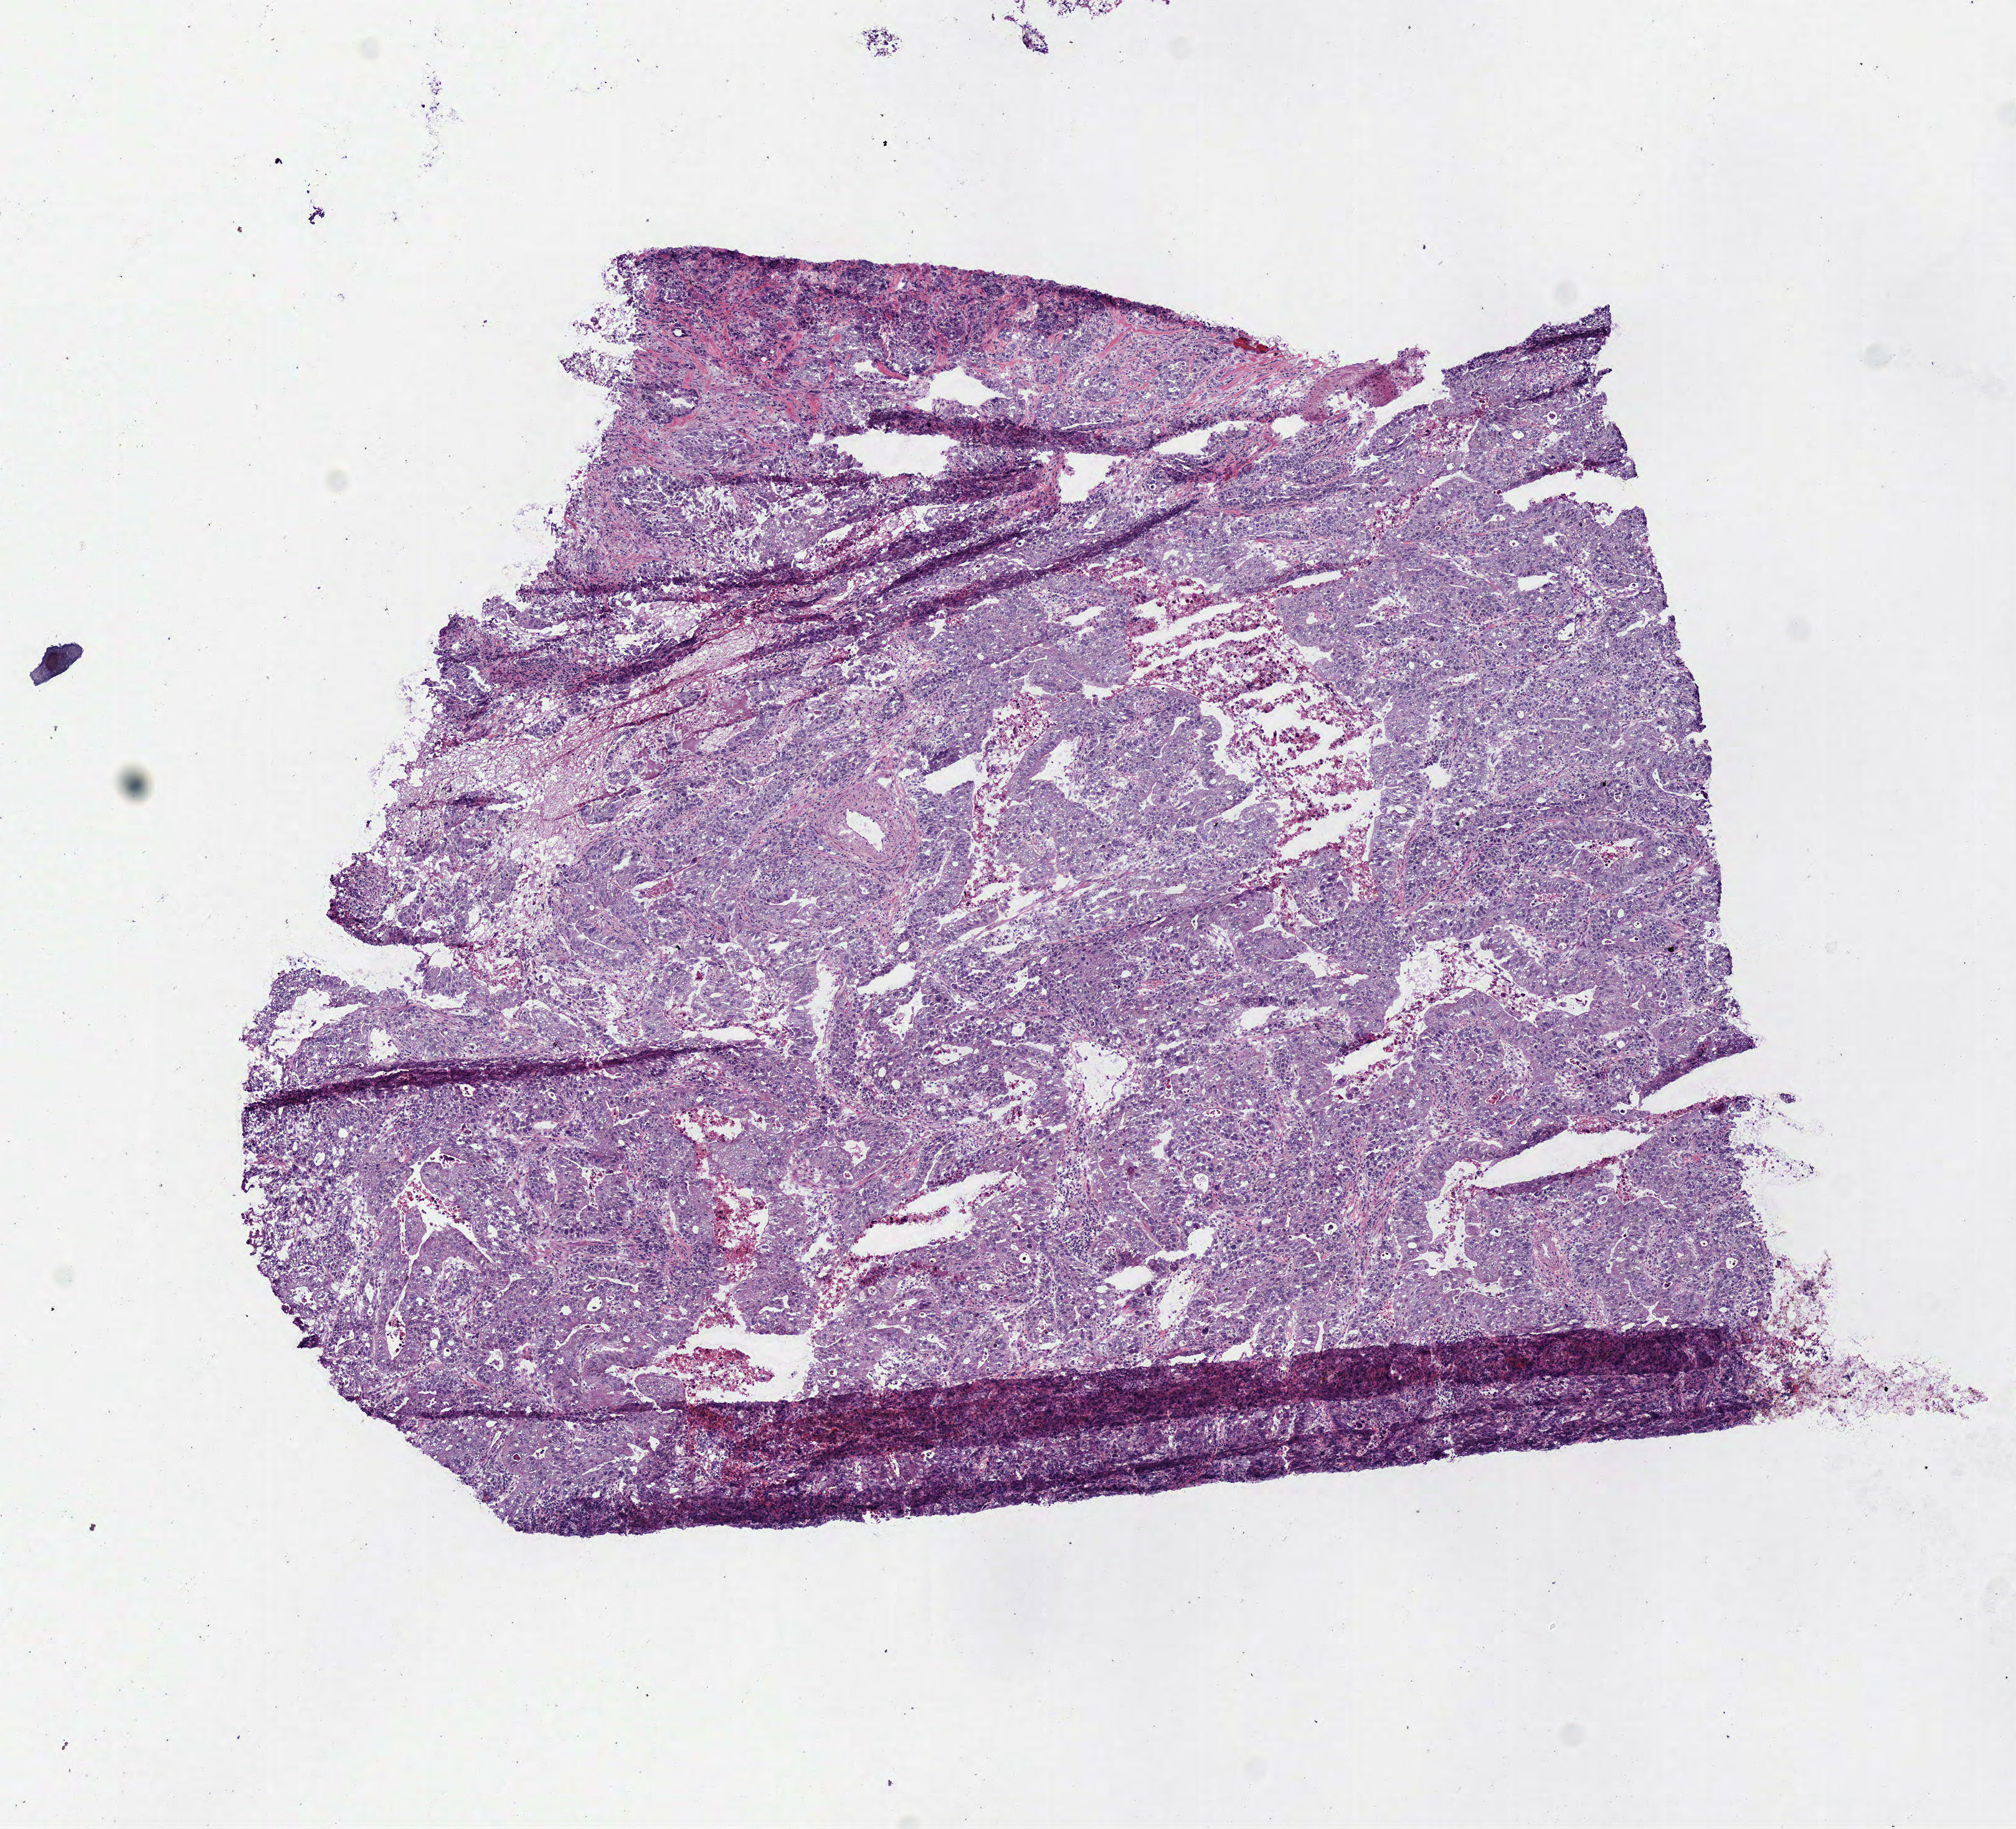
H&E-stained whole-slide image, whole scanned area (about 6.4 x 5.8 mm, from a 40x scan) shown as a low-resolution overview. Frozen section from the bottom of the tissue portion. Primary tumour sample from the stomach. Female patient; age at initial diagnosis 67 years. Histologic grade: G2 (moderately differentiated). Composition of this section per pathologist review: tumour cells 80%, tumour nuclei 80%, normal cells 0%, stromal cells 10%, necrosis 10%.
Lymph nodes positive (case pathology): 3 of 19 examined. AJCC pathologic stage: IIIA. Pathologic diagnosis: Tubular adenocarcinoma (body of stomach).